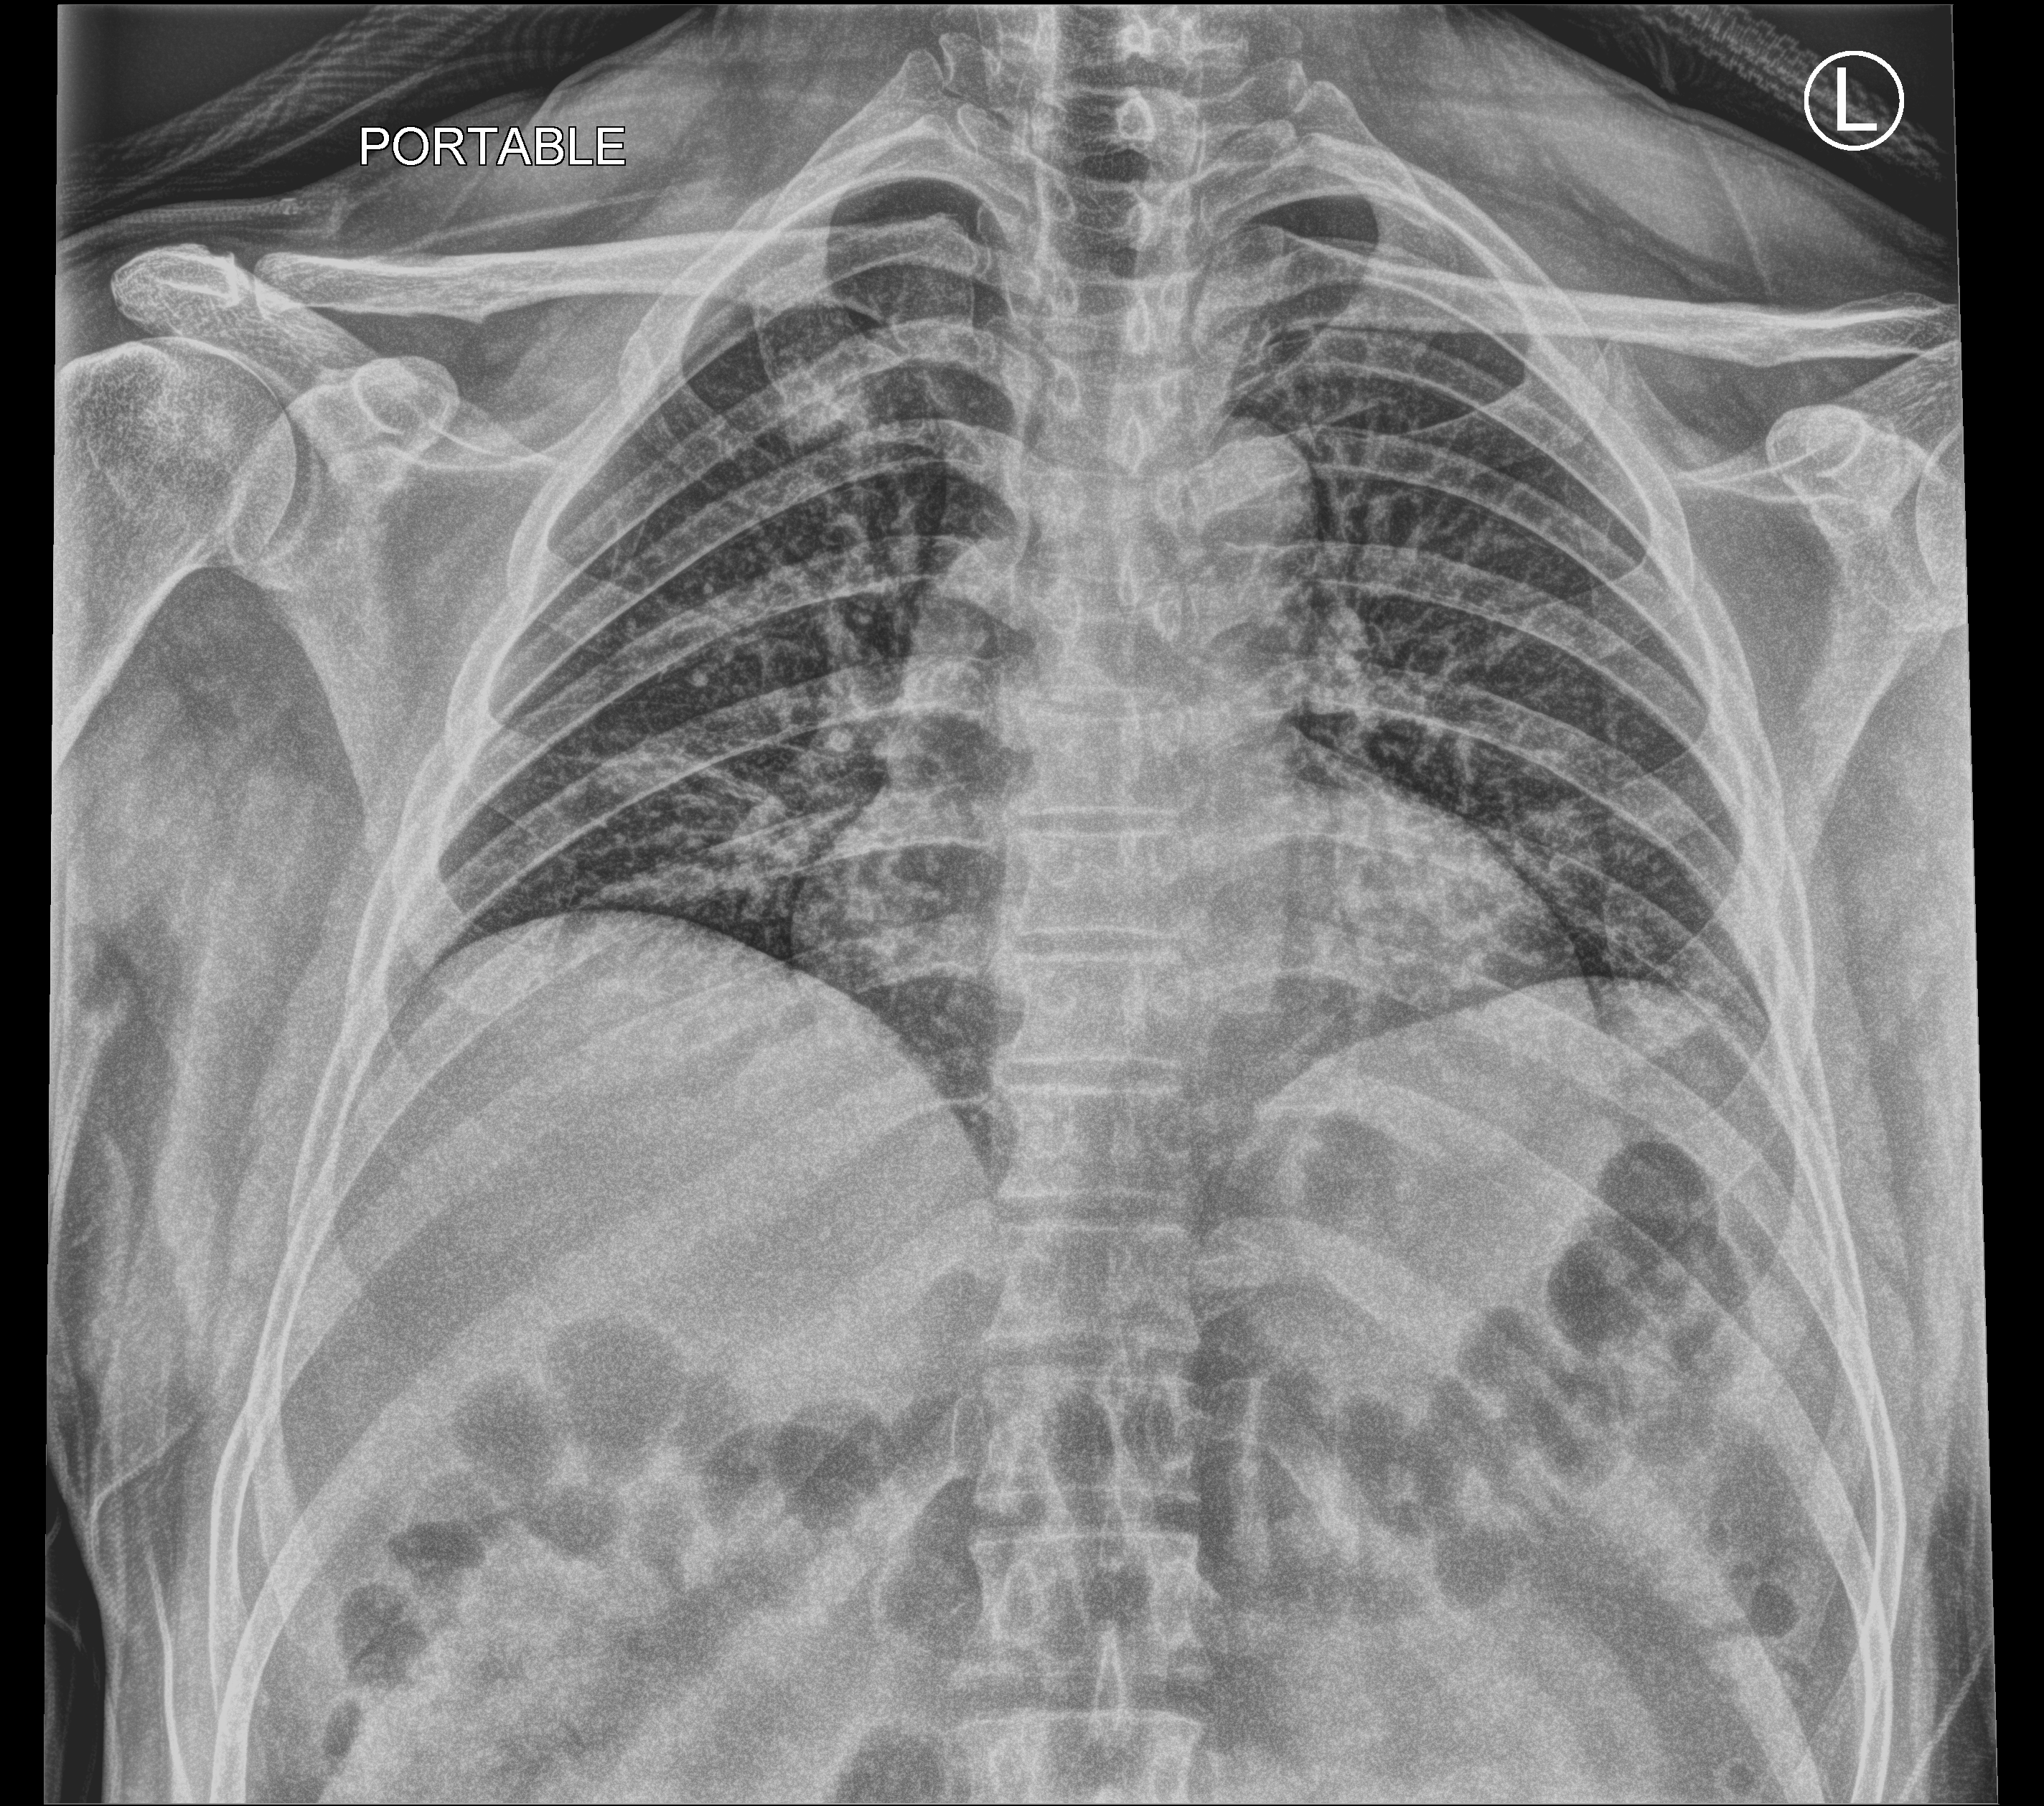
Bedside chest radiograph (computed radiography); anteroposterior (AP) projection. Patient hospitalised with COVID-19; male, aged 18–59 years.
Admission-level facts for this patient (not findings on this image; timing relative to this image not recorded): other chronic lung disease (admission record): no; hypertension (admission record): no; mechanically ventilated during this hospital stay: no.